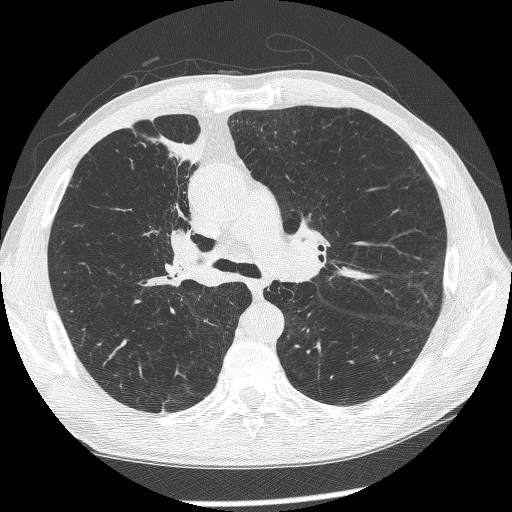
Axial slice from a low-dose chest CT screening exam, baseline screening round, lung window (W 1500 / L -600 HU), 1.25 mm slice thickness, lung (sharp) reconstruction kernel (BONE), 512 × 512 image matrix, field of view 340 × 340 mm. Male, age 60 years at enrolment. Current smoker at enrolment.
Expert reader's lesion annotation, bounding box <144,201,223,294> (left, top, right, bottom; pixels). The exam's reader record, not a measurement of the box and not confirmed to be the same lesion: non-calcified nodule or mass ≥4 mm, right upper lobe, 12 × 8 mm, spiculated (stellate) margins, mixed attenuation. Official screen result: positive, change unspecified: nodule(s) >= 4 mm or enlarging nodule(s), mass(es), or other non-specific abnormalities suspicious for lung cancer. Later outcome: lung cancer diagnosed 208 days after this screen — squamous cell carcinoma, NOS, right upper lobe, right middle lobe, right main stem bronchus, poorly differentiated (G3), stage IV (AJCC 6th edition).